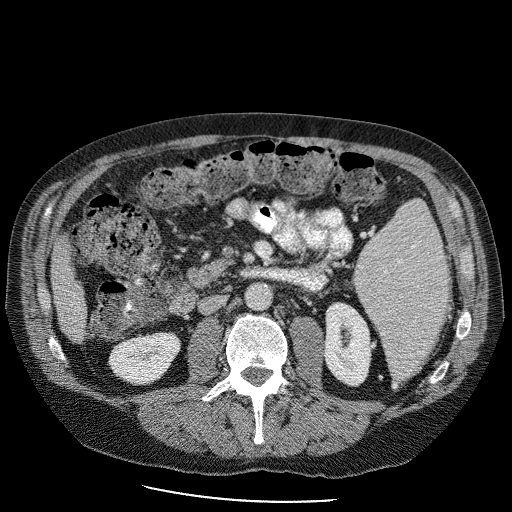
Contrast-enhanced abdominal CT (liver protocol), one axial slice; slice 25 of 98 in the series (ordered by position); reconstruction kernel STANDARD; 120 kVp; soft-tissue window (W 400 / L 40 HU); 512 × 512 image matrix, field of view 400 × 400 mm. Case-level facts recorded for this patient, not image findings: diagnosis: hepatocellular carcinoma (patient treated with transarterial chemoembolisation; whether this scan precedes or follows treatment is not stated here); TNM stage (as recorded): Stage-II; Child-Pugh class: B; tumour nodularity: uninodular.
Annotated regions visible in this slice (semi-automatic segmentation, software-assisted and operator-edited):
- liver parenchyma outside the tumour (the mass and vessels are separate outlines, so this box may not span the whole liver): bounding box (x1, y1, x2, y2) in pixels: (50, 224, 89, 342)